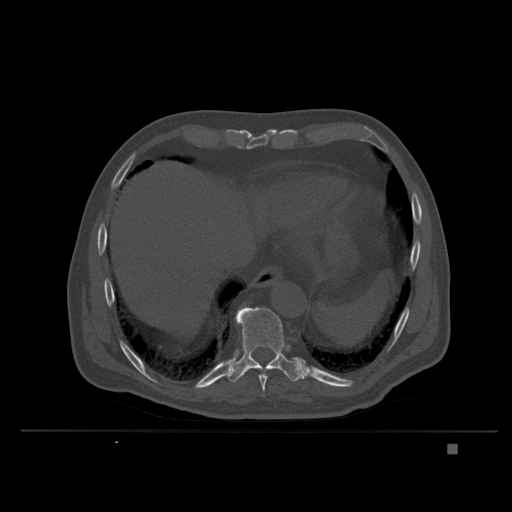
CT including the spine, one axial slice; position 199 of 435 along the scan axis; bone window (W 1800 / L 400 HU); 1.5 mm slice thickness; 512 × 512 image matrix, field of view 434 × 434 mm. Patient: male, 73 years. Case-level facts recorded for this patient, not image findings: primary cancer: skin.
Annotated regions visible in this slice (semi-automatic segmentation, software-assisted and operator-edited):
- T10 vertebra: bounding box [x1, y1, x2, y2] px = [227, 304, 305, 383]
- T9 vertebra: [258, 366, 271, 397]